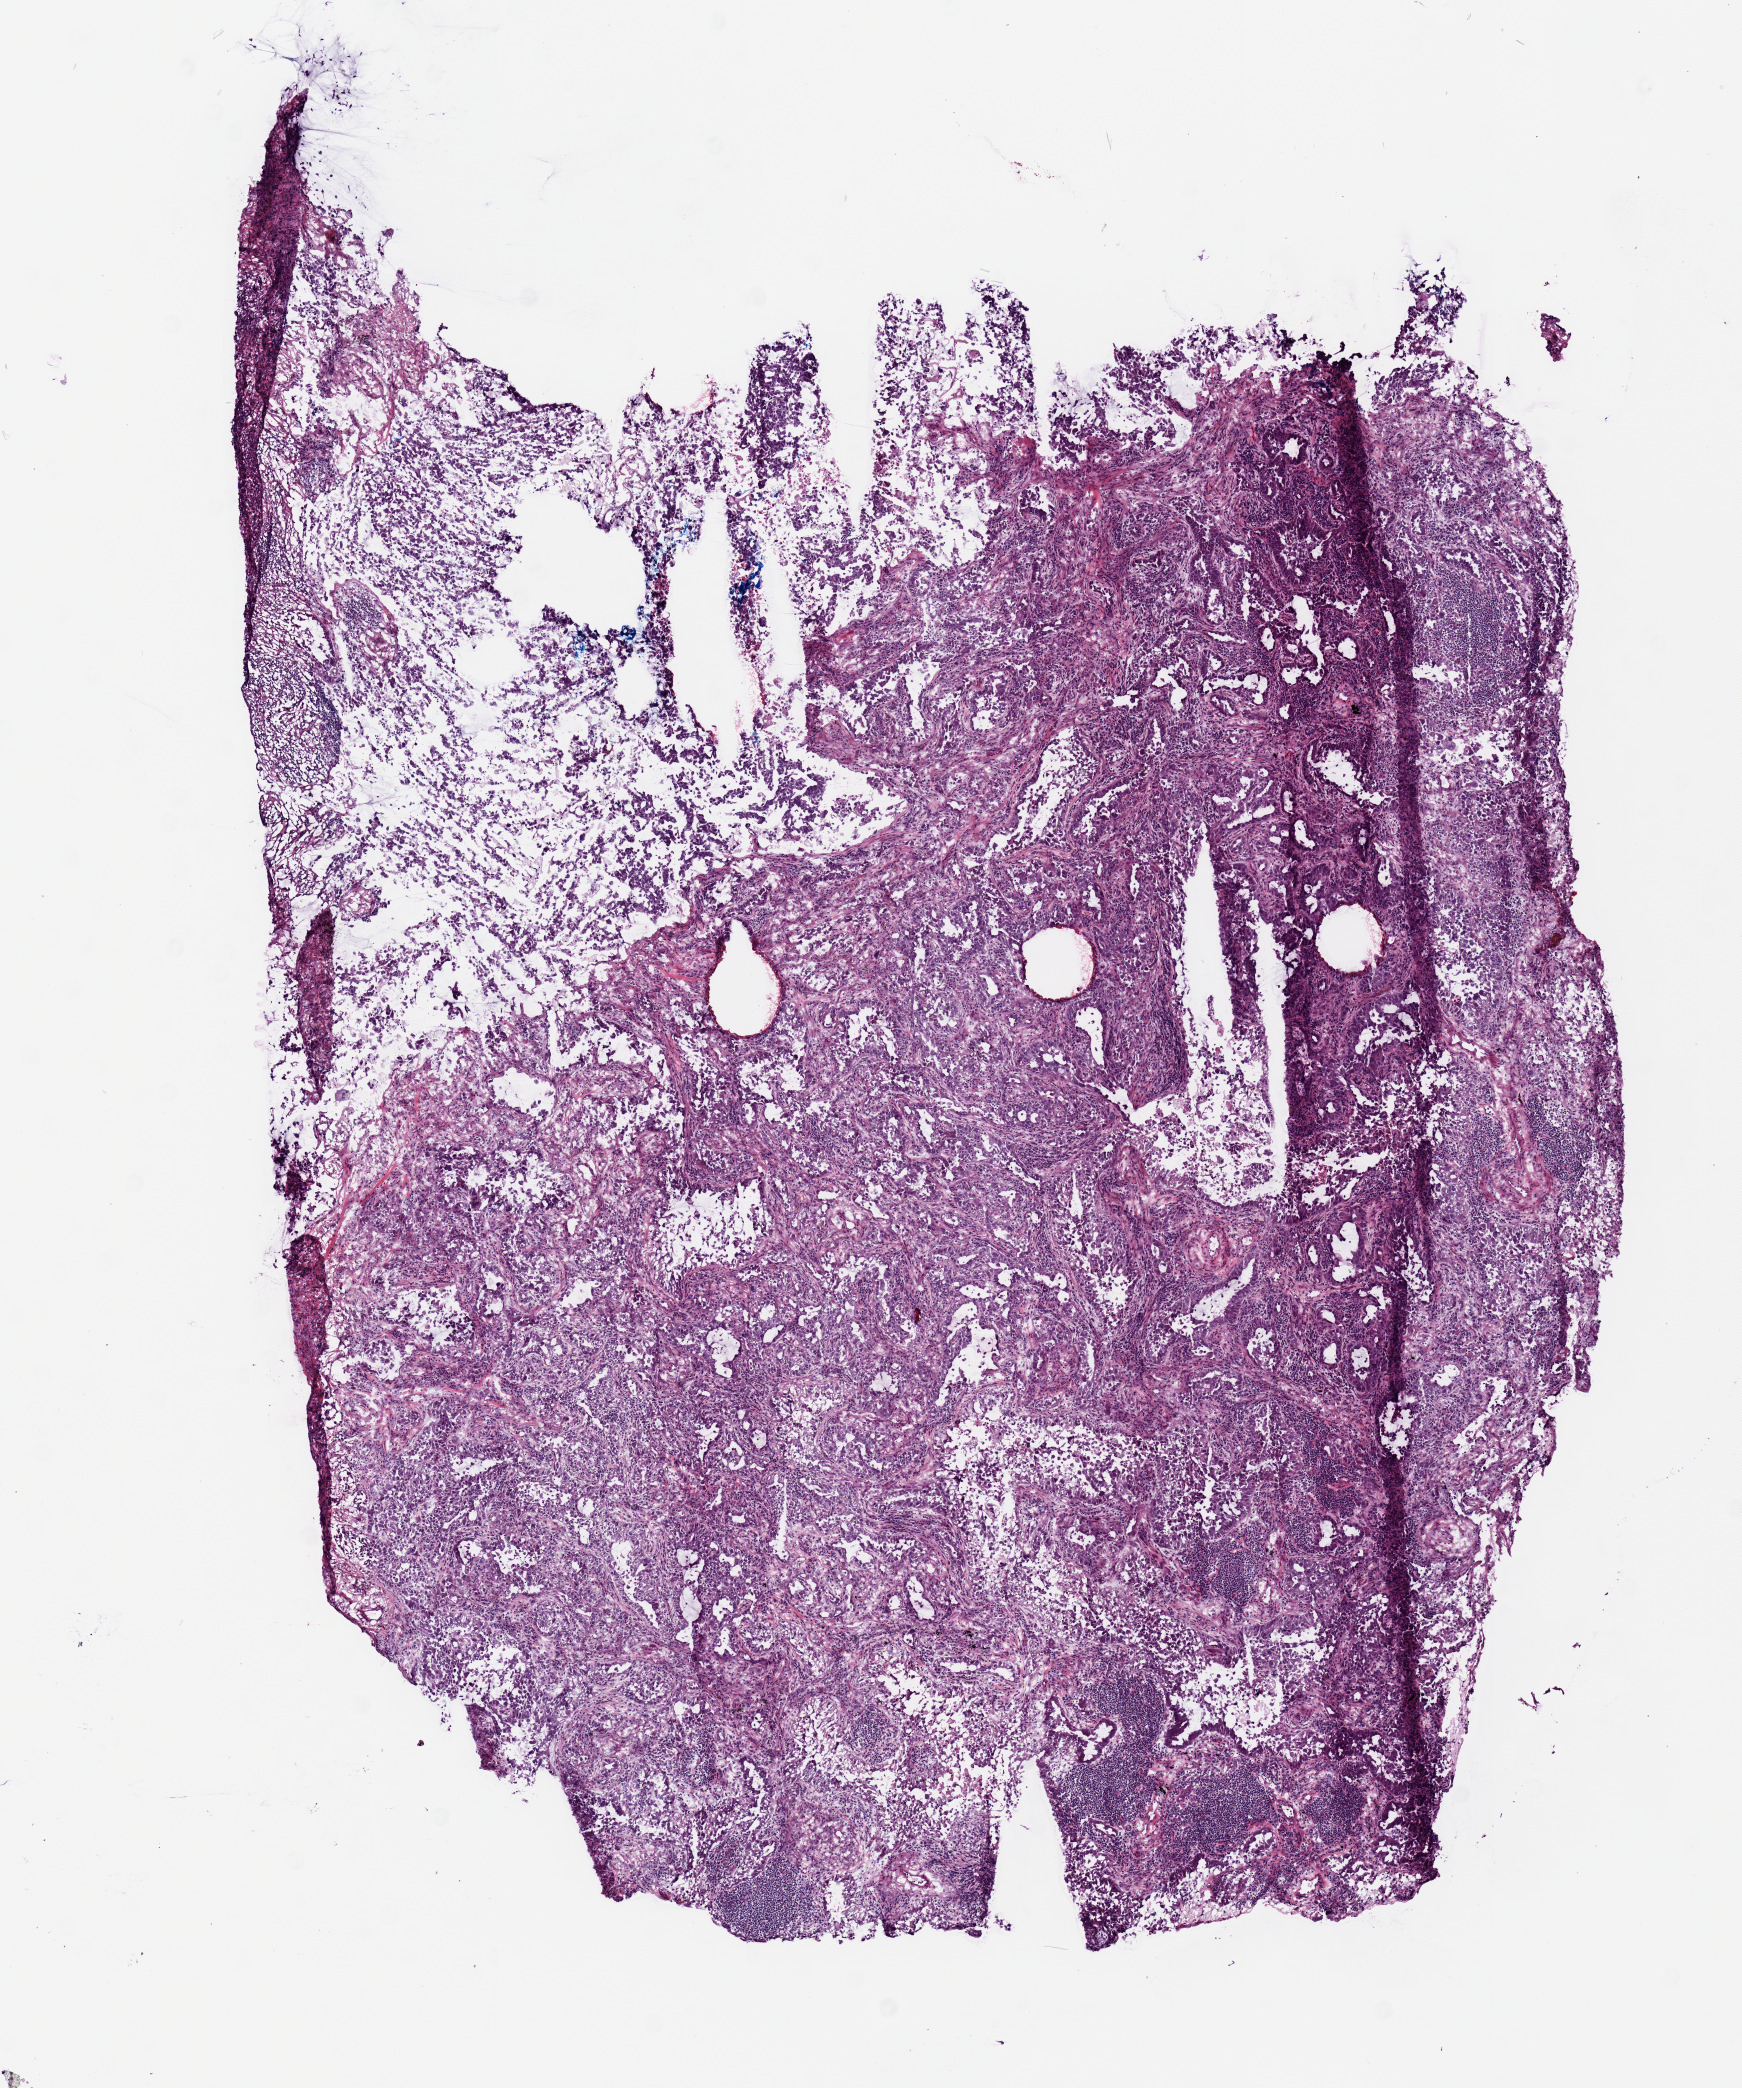
Whole-slide histology image, Hematoxylin and eosin (H&E) stained — shown as a low-resolution overview of the whole scanned area (about 6.9 x 8.3 mm, acquisition: 20x scan); frozen section; primary tumour sample from the lung. Female patient; age at initial diagnosis 81 years. Pathologist review of this section (percent, as recorded): tumour cells 73%, tumour nuclei 65%, normal cells 0%, stromal cells 10%, necrosis 12%. Inflammatory infiltration, as recorded: lymphocyte infiltration 0%, monocyte infiltration 0%, neutrophil infiltration 0%.
AJCC pathologic stage: IA (7th edition). Histologic diagnosis: Adenocarcinoma, NOS (lower lobe, lung).